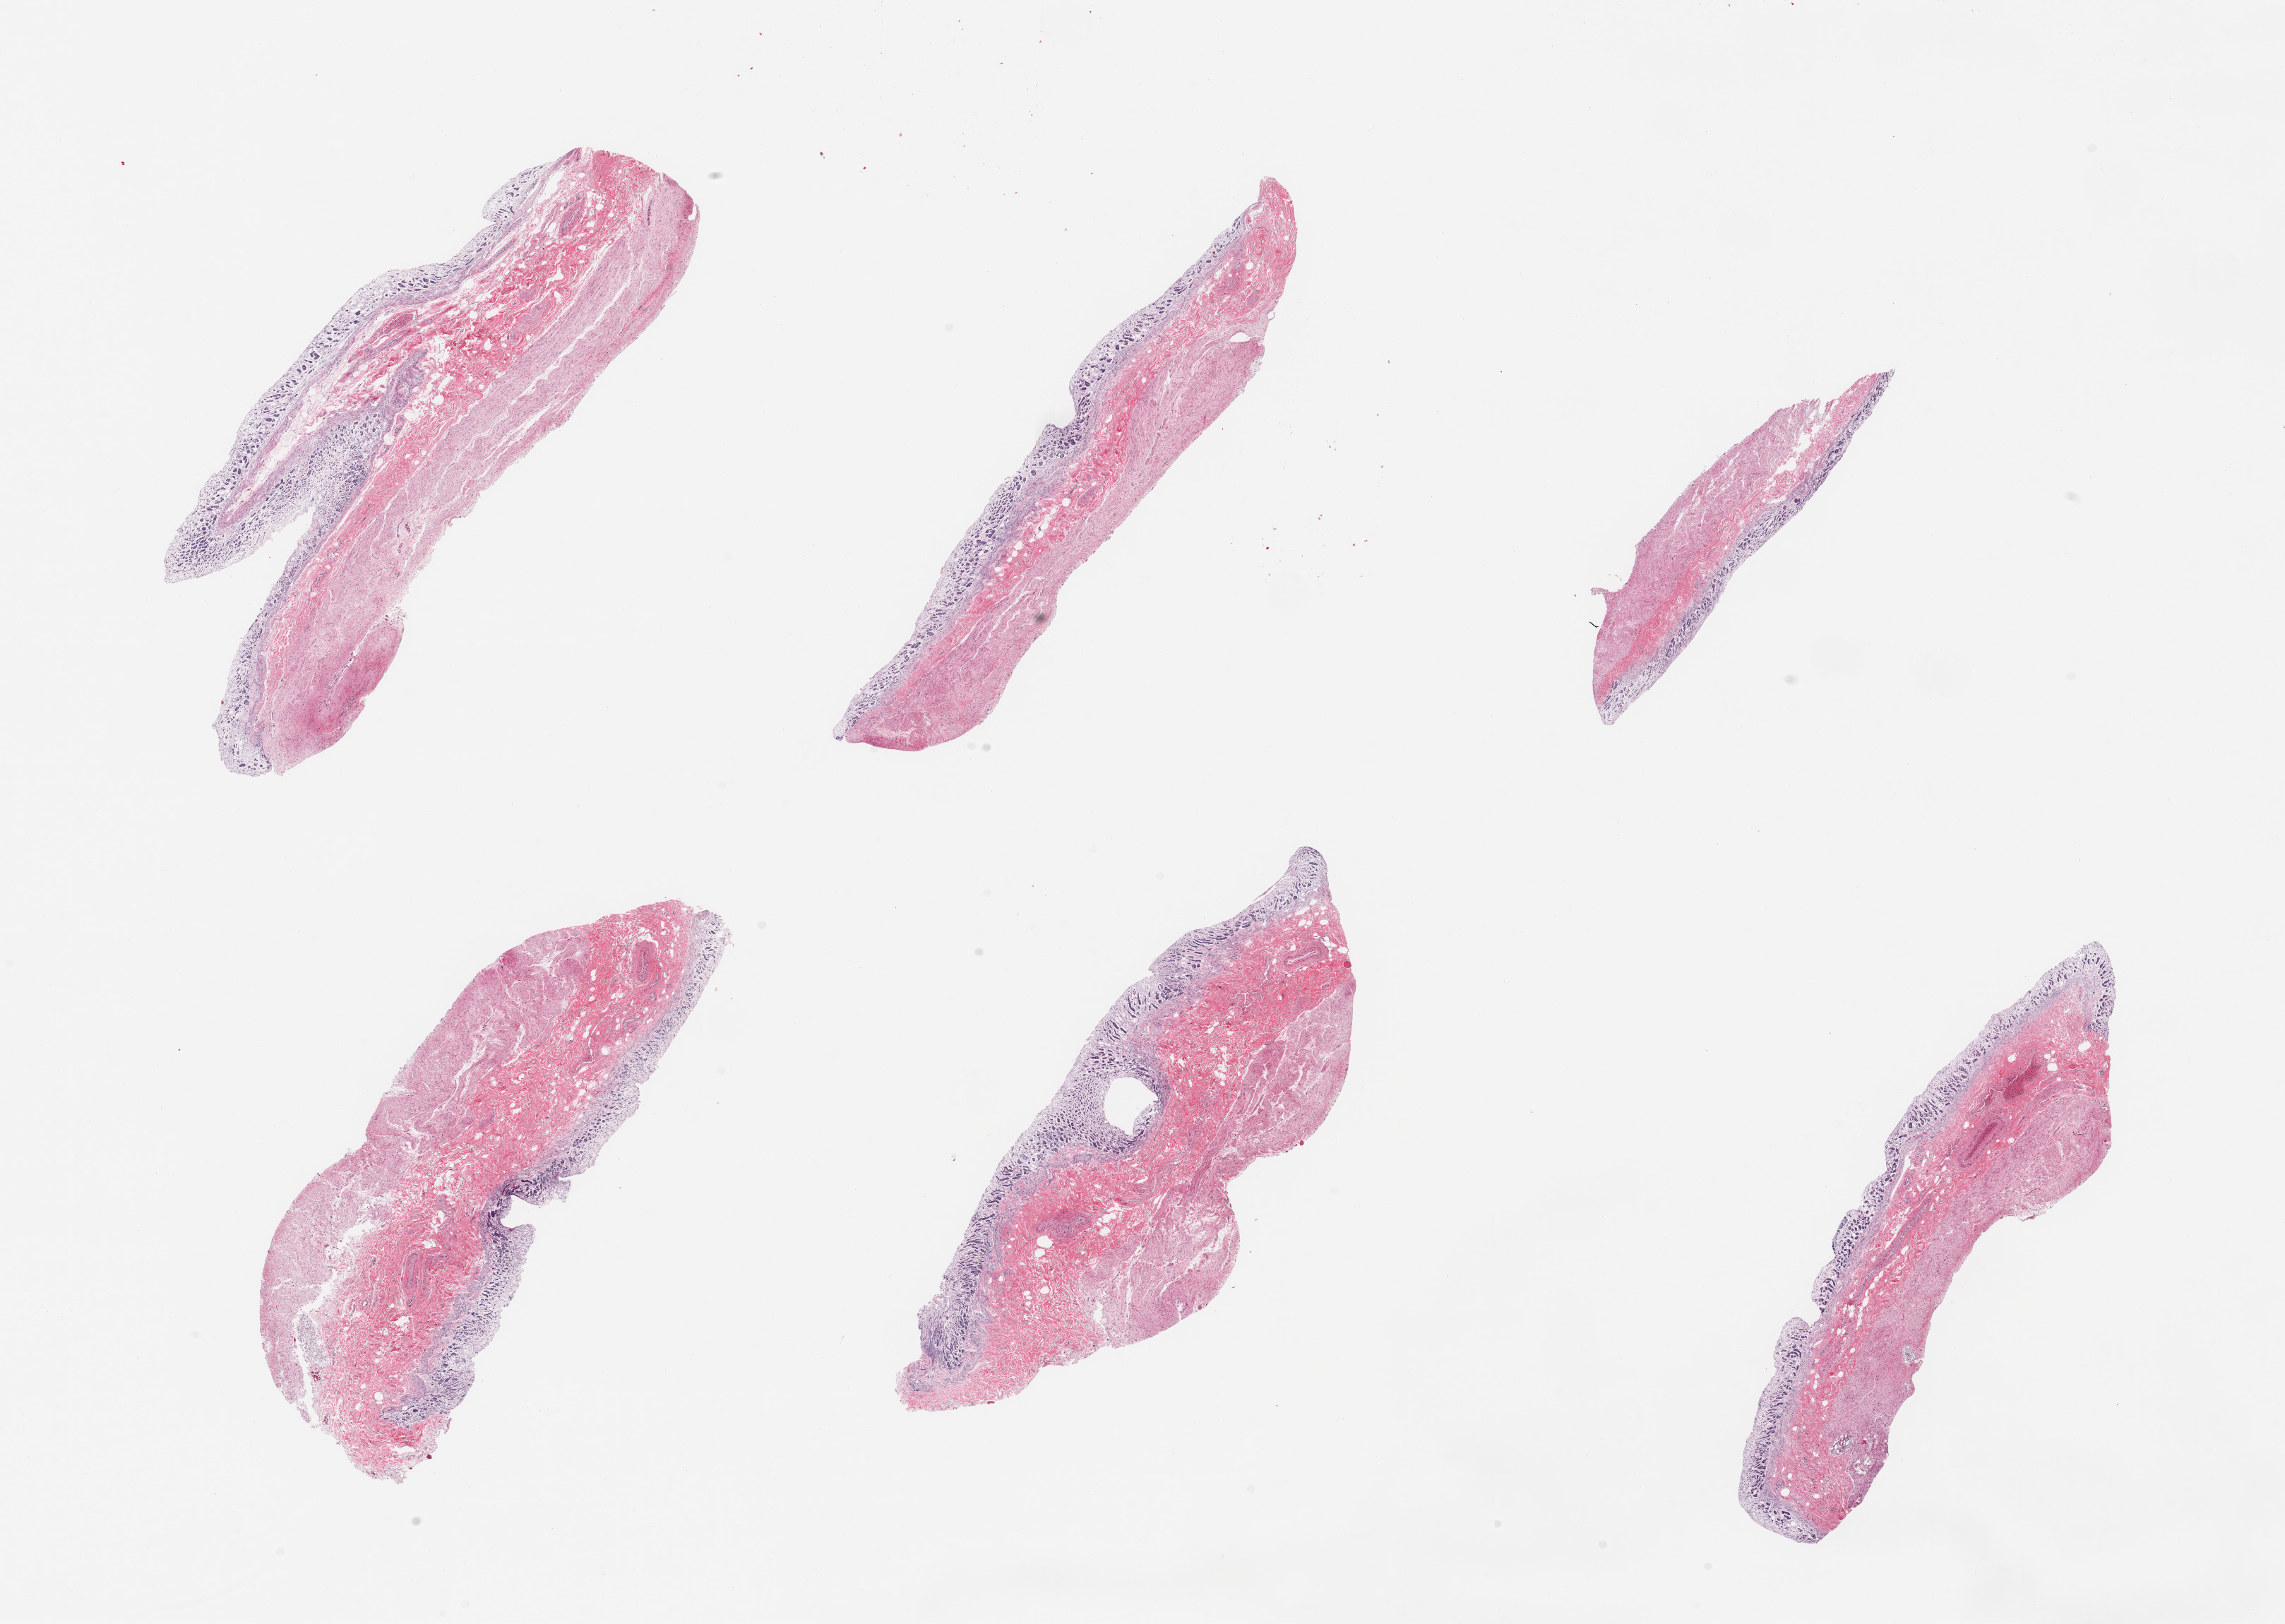
Digitized H&E-stained section, brightfield, whole scanned area (about 25.6 x 18.2 mm) shown as a low-resolution overview, PAXgene-fixed, paraffin-embedded tissue, section of stomach (target tissue), tissue donor sample. Donor: male.
Review note (as recorded): 6 pieces, target mucosa up to ~0.3mm, completely autolyzed.